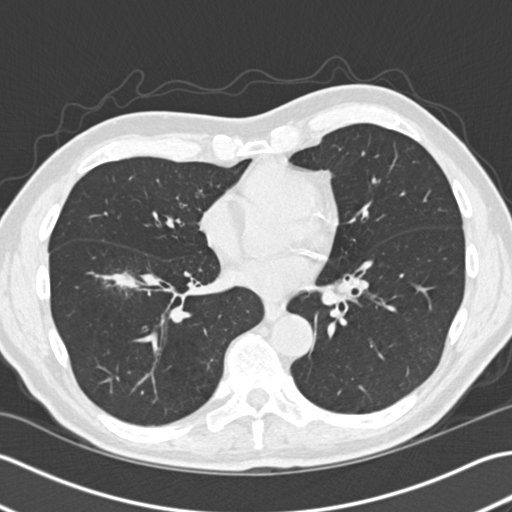
Low-dose screening chest CT, one axial slice. Slice 73 of 172 in the series (ordered by position). Reconstruction kernel B30f. 120 kVp. Lung window (W 1500 / L -600 HU). 2 mm slice thickness. 512 × 512 image matrix.
Outlined on this slice (manually delineated by an expert):
- lesion 1 (tumor, lower lobe of right lung): bounding box [x1, y1, x2, y2] px = [102, 272, 141, 290]